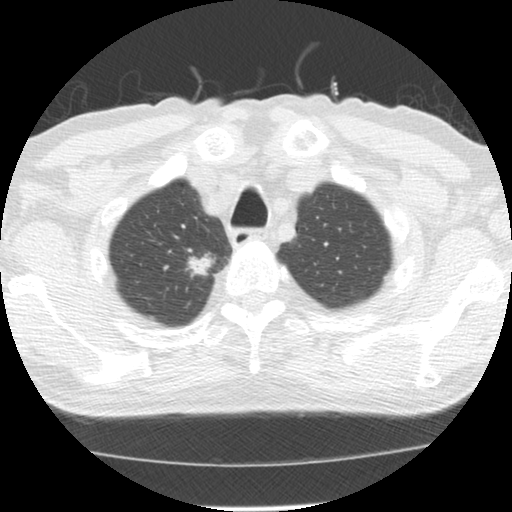
Low-dose screening chest CT, axial slice. First (baseline) screen. Lung window (W 1500 / L -600 HU). Standard (soft-tissue) reconstruction kernel (STANDARD). Slice 24 of 139 in the series. 512 × 512 image matrix. Male, age 64 years at enrolment. Former smoker at enrolment.
Lesion marked by an expert reader, box from (x=179, y=240) to (x=224, y=281) px. Reader record for this screening exam (exam-level; its link to the box is not recorded): non-calcified nodule or mass ≥4 mm, right upper lobe, 20 × 13 mm, spiculated (stellate) margins, soft tissue attenuation. Official screen result: positive, change unspecified: nodule(s) >= 4 mm or enlarging nodule(s), mass(es), or other non-specific abnormalities suspicious for lung cancer. Participant outcome: lung cancer diagnosed 73 days after this screen — adenocarcinoma, NOS, right upper lobe, moderately differentiated (G2), stage IA (AJCC 6th edition), 17 mm at pathology.